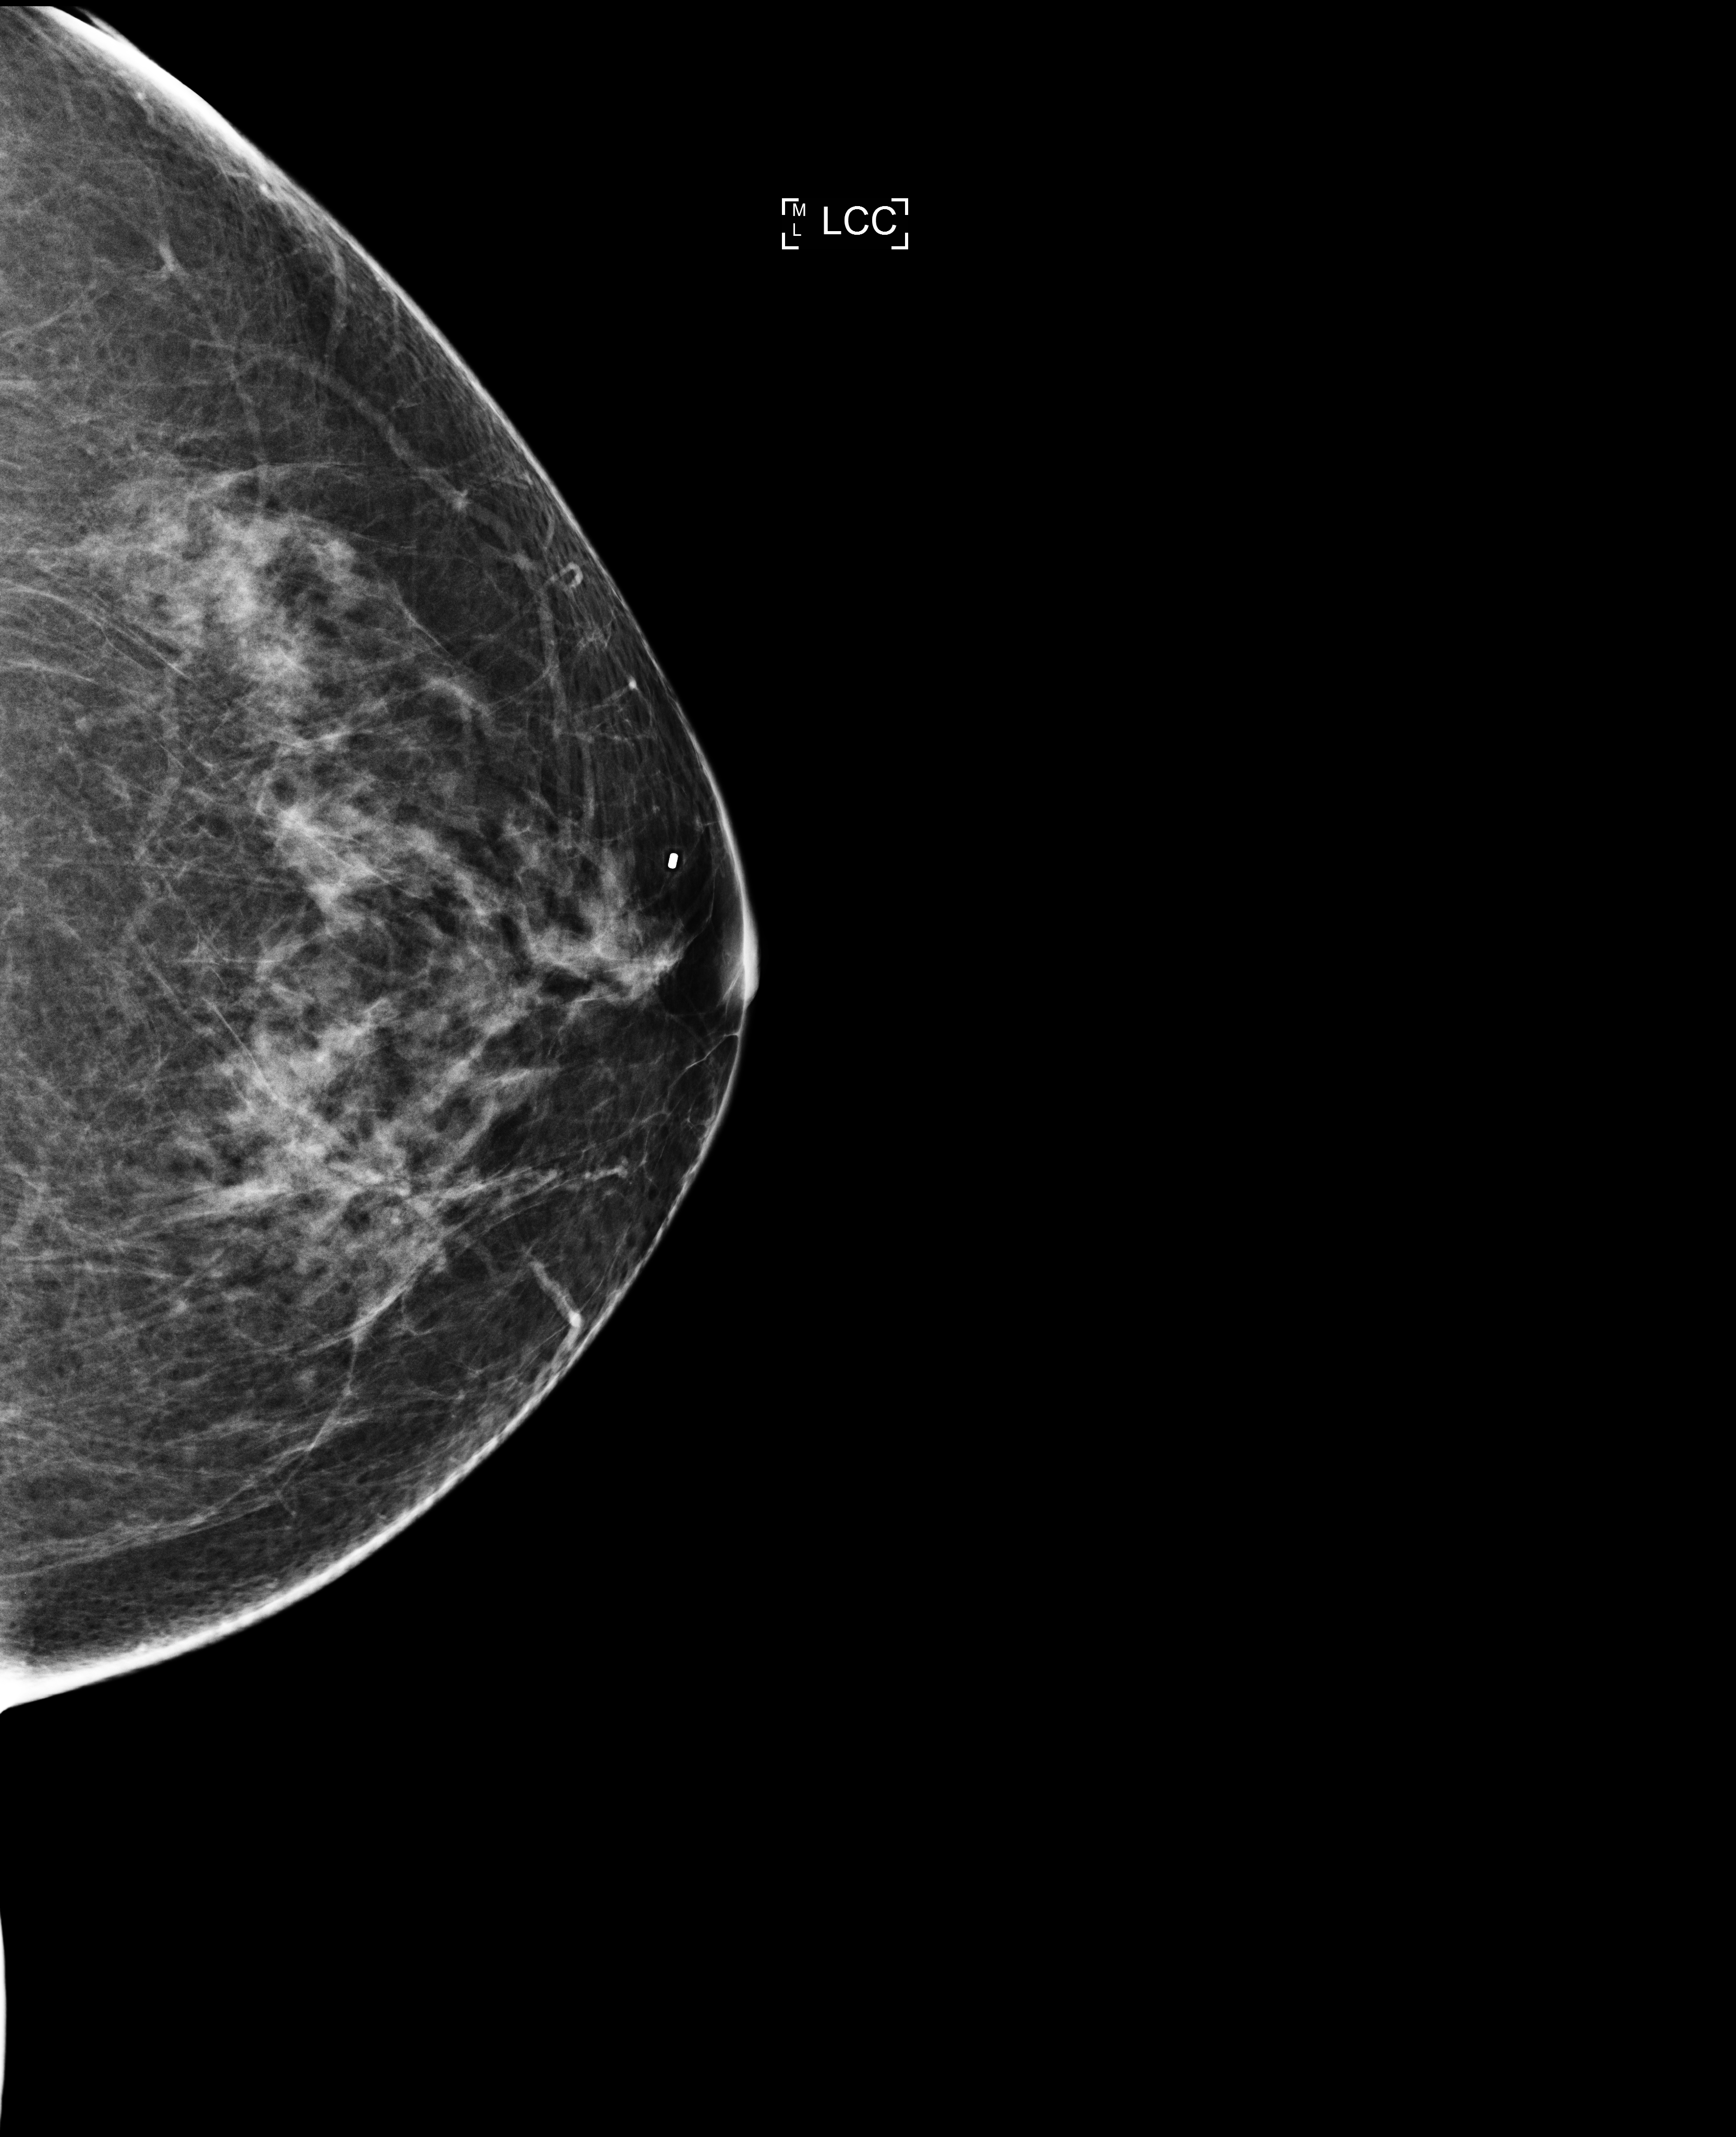
Full-field digital mammogram (FFDM), left breast, cranio-caudal projection, screening examination. Patient: female, 56 years.
Breast density at the screening exam (both breasts): scattered fibroglandular densities (BI-RADS density category b). Final BI-RADS assessment for this screening round (tomosynthesis exam, both breasts): category 1. Recall: no recall after this screen.